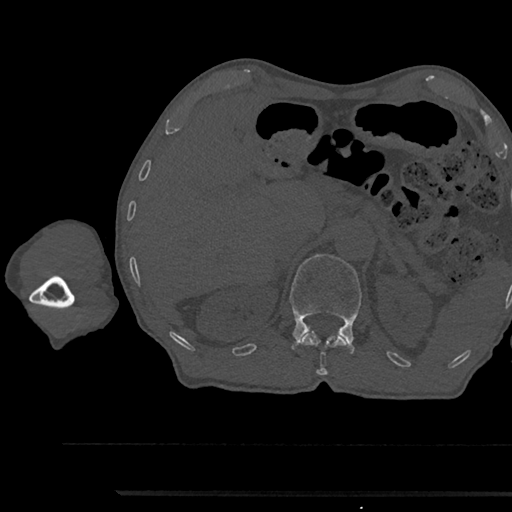
CT including the spine, one axial slice; position 672 of 797 along the scan axis; reconstruction kernel Br40s/3; 120 kVp; bone window (W 1800 / L 400 HU); 512 × 512 image matrix. Male patient, age 79 years. Case-level facts recorded for this patient, not image findings: primary cancer: prostate.
Outlined on this slice (semi-automatic segmentation, software-assisted and operator-edited):
- L1 vertebra: bounding box [x1, y1, x2, y2] px = [290, 254, 362, 353]
- T12 vertebra: [246, 331, 352, 375]